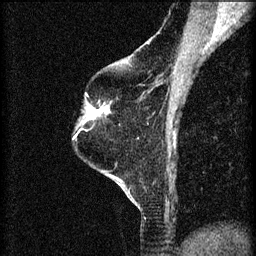
Breast MRI (dynamic contrast-enhanced), one sagittal slice. Position 46 of 60 along the scan axis. 3 images stored at this slice position (order not interpretable as contrast timing). 1.5 T. TE 4.2 ms, TR 8.2 ms. 256 × 256 image matrix, field of view 180 × 180 mm. Patient: female, 60 years.
Annotated regions visible in this slice (semi-automatic segmentation, software-assisted and operator-edited):
- analysis volume of interest (the breast-tissue region the enhancement analysis was run in; not a lesion): bounding box (x1, y1, x2, y2) in pixels: (78, 94, 108, 129)
- tumour enhancement mask (voxels above the 70 % enhancement threshold inside the analysis volume of interest): (86, 106, 108, 121)